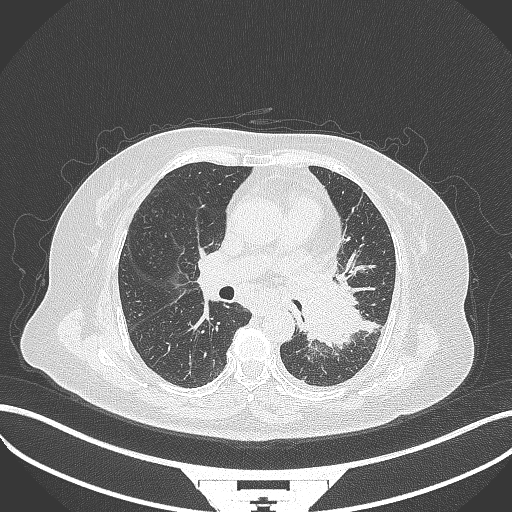
Chest CT, one axial slice; 120 kVp; lung window (W 1500 / L -600 HU); 1 mm slice thickness; 512 × 512 image matrix. Patient: female, 69 years. Case-level facts recorded for this patient, not image findings: clinical TNM (as recorded): T2b N3 M1.
Outlined on this slice (rectangle marked by the reading radiologist):
- lung tumour (recorded histology: adenocarcinoma): bounding box [x1, y1, x2, y2] px = [297, 268, 362, 351]